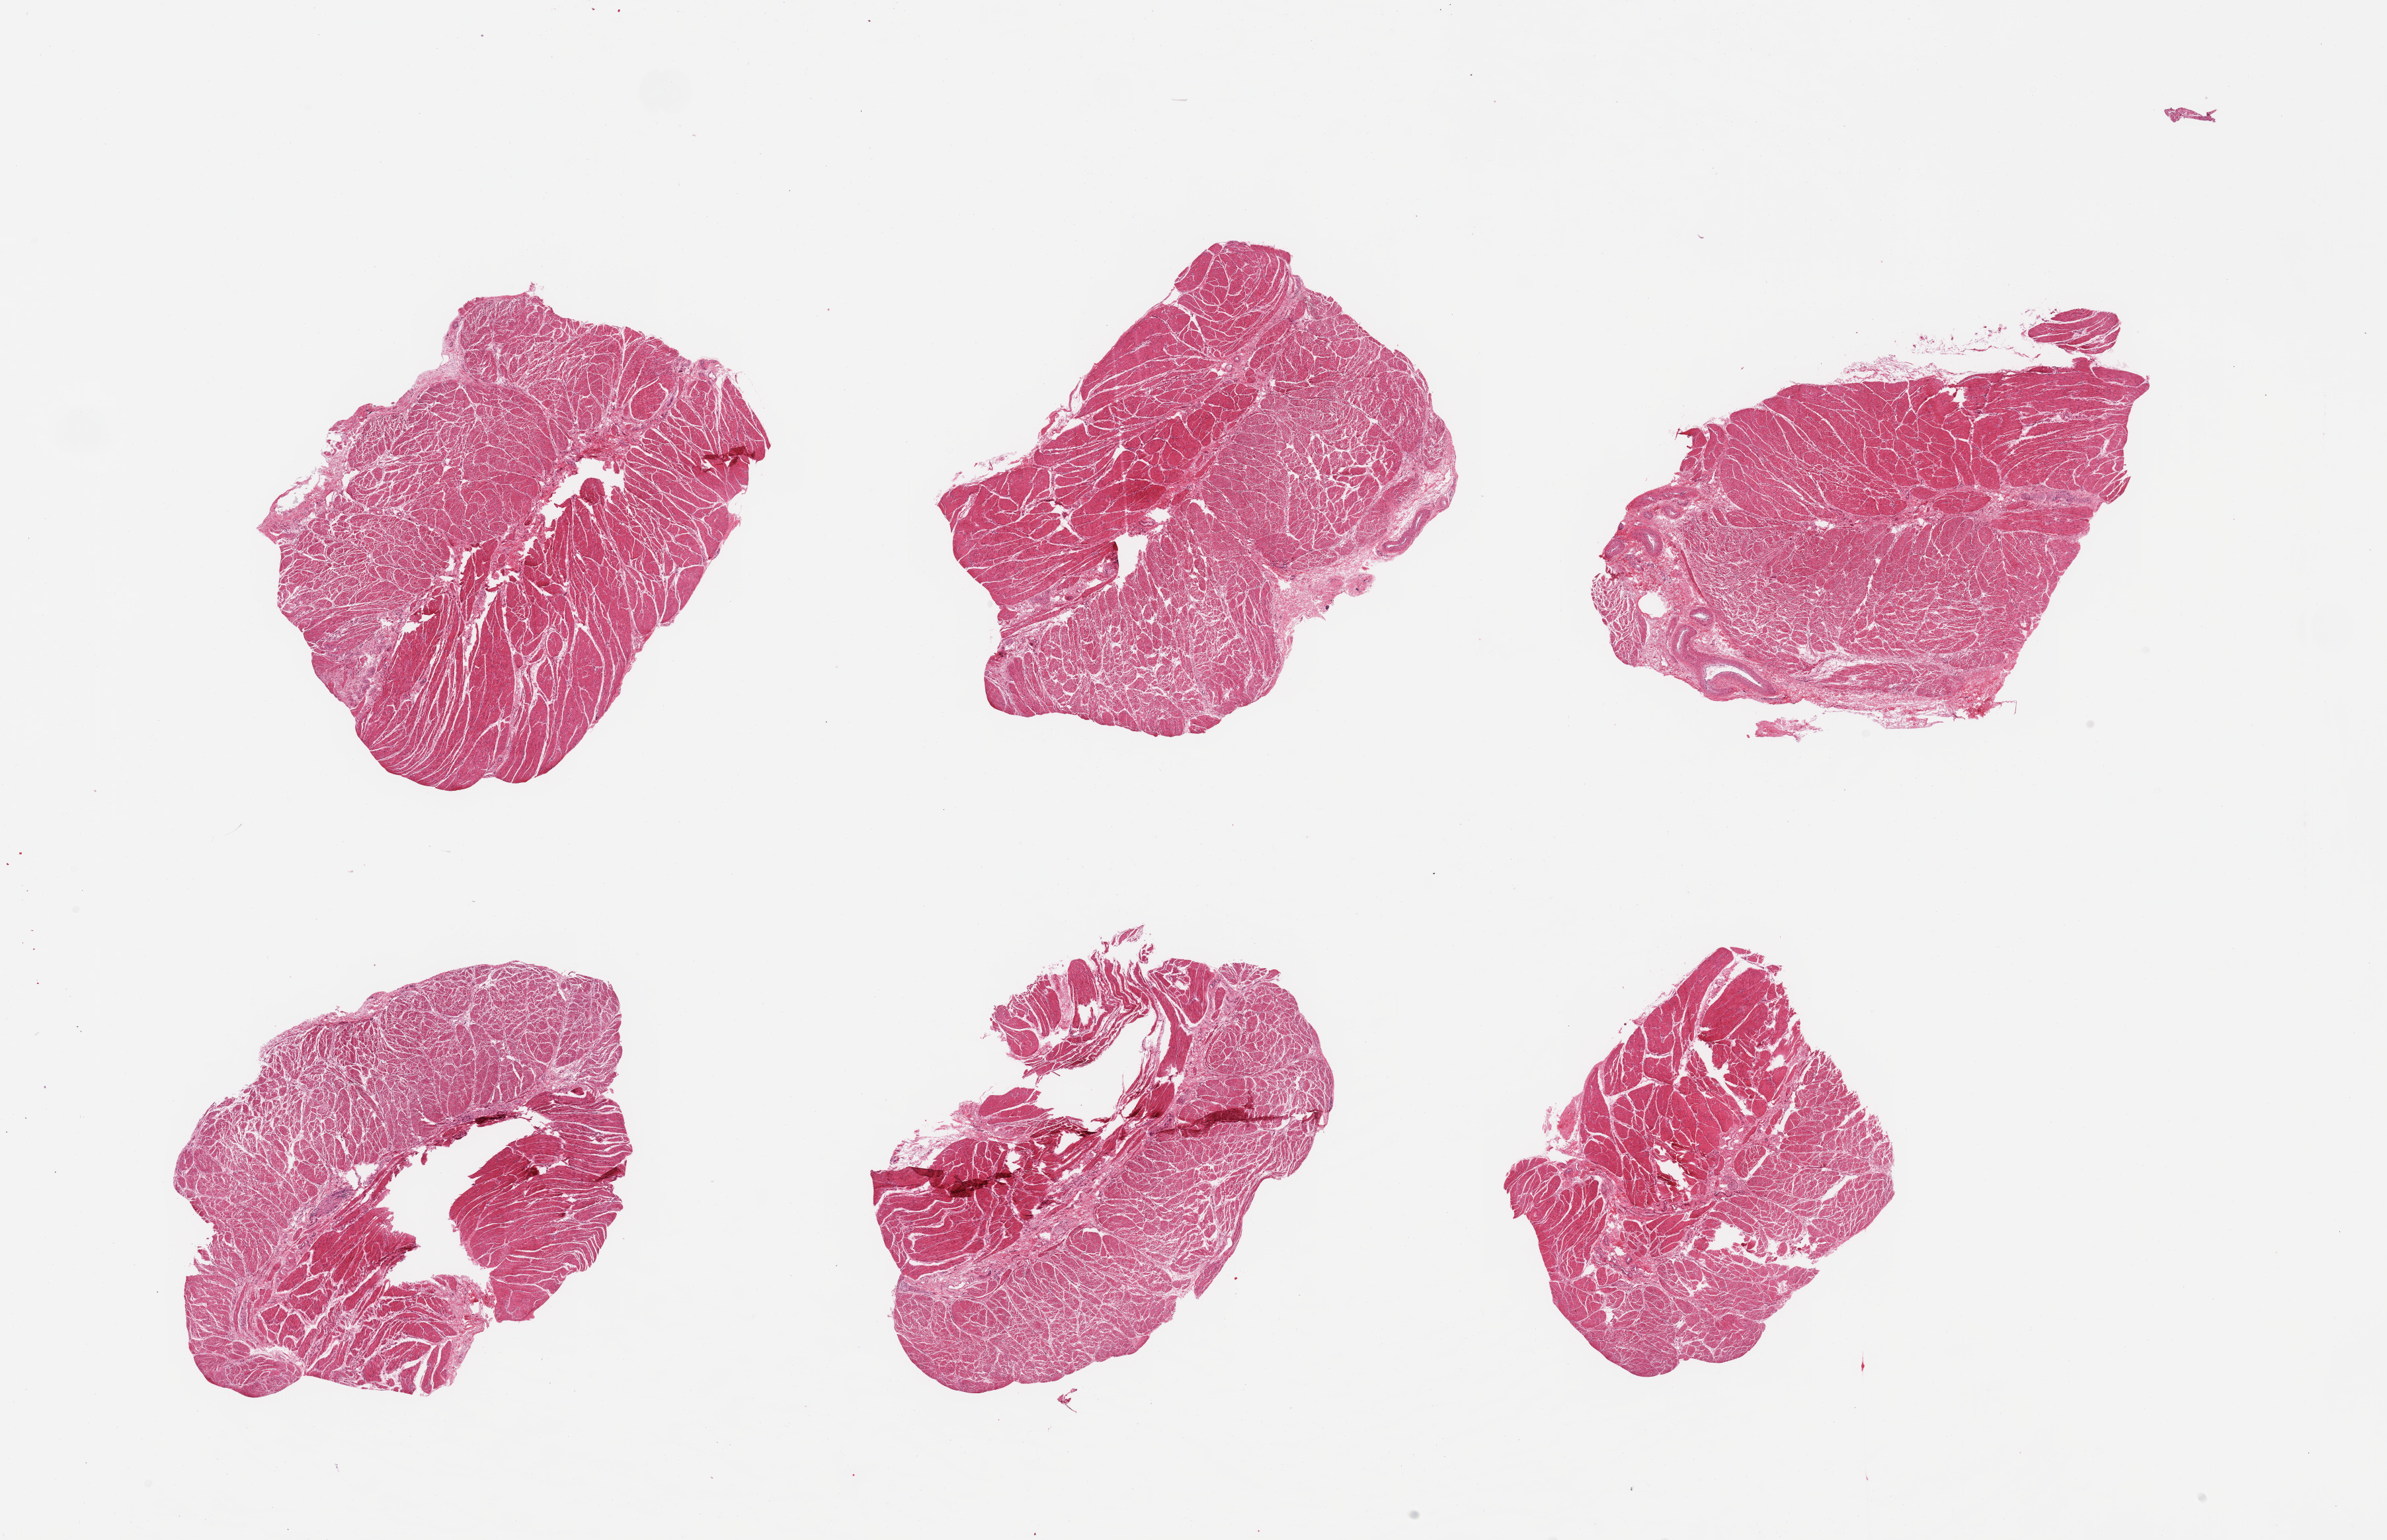
Haematoxylin and eosin whole-slide image, low-resolution overview of the scanned area, about 28.5 x 18.4 mm; PAXgene-fixed, paraffin-embedded tissue; target tissue: esophageal muscle; donor tissue sample. Donor: male.
Pathologist's review note for this sample: 6 pieces, confirmed target muscularis.